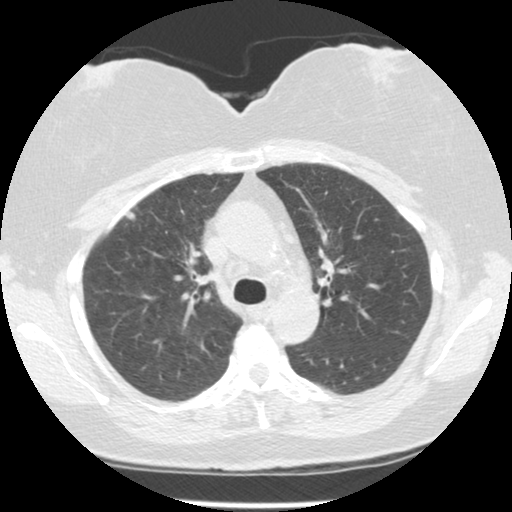
Axial slice from a low-dose chest CT screening exam, third screening round (two years after baseline), lung window (W 1500 / L -600 HU), 2.5 mm slice thickness, standard (soft-tissue) reconstruction kernel (STANDARD), slice 87 of 122 in the series. Female, age 59 years at enrolment.
Lesion marked by an expert reader, bounding box <115,202,144,227> (left, top, right, bottom; pixels). No non-calcified nodule or mass ≥4 mm was recorded by the screening reader at this exam. Later outcome: lung cancer diagnosed 349 days after this screen — small cell carcinoma, NOS, stage IV (AJCC 6th edition).